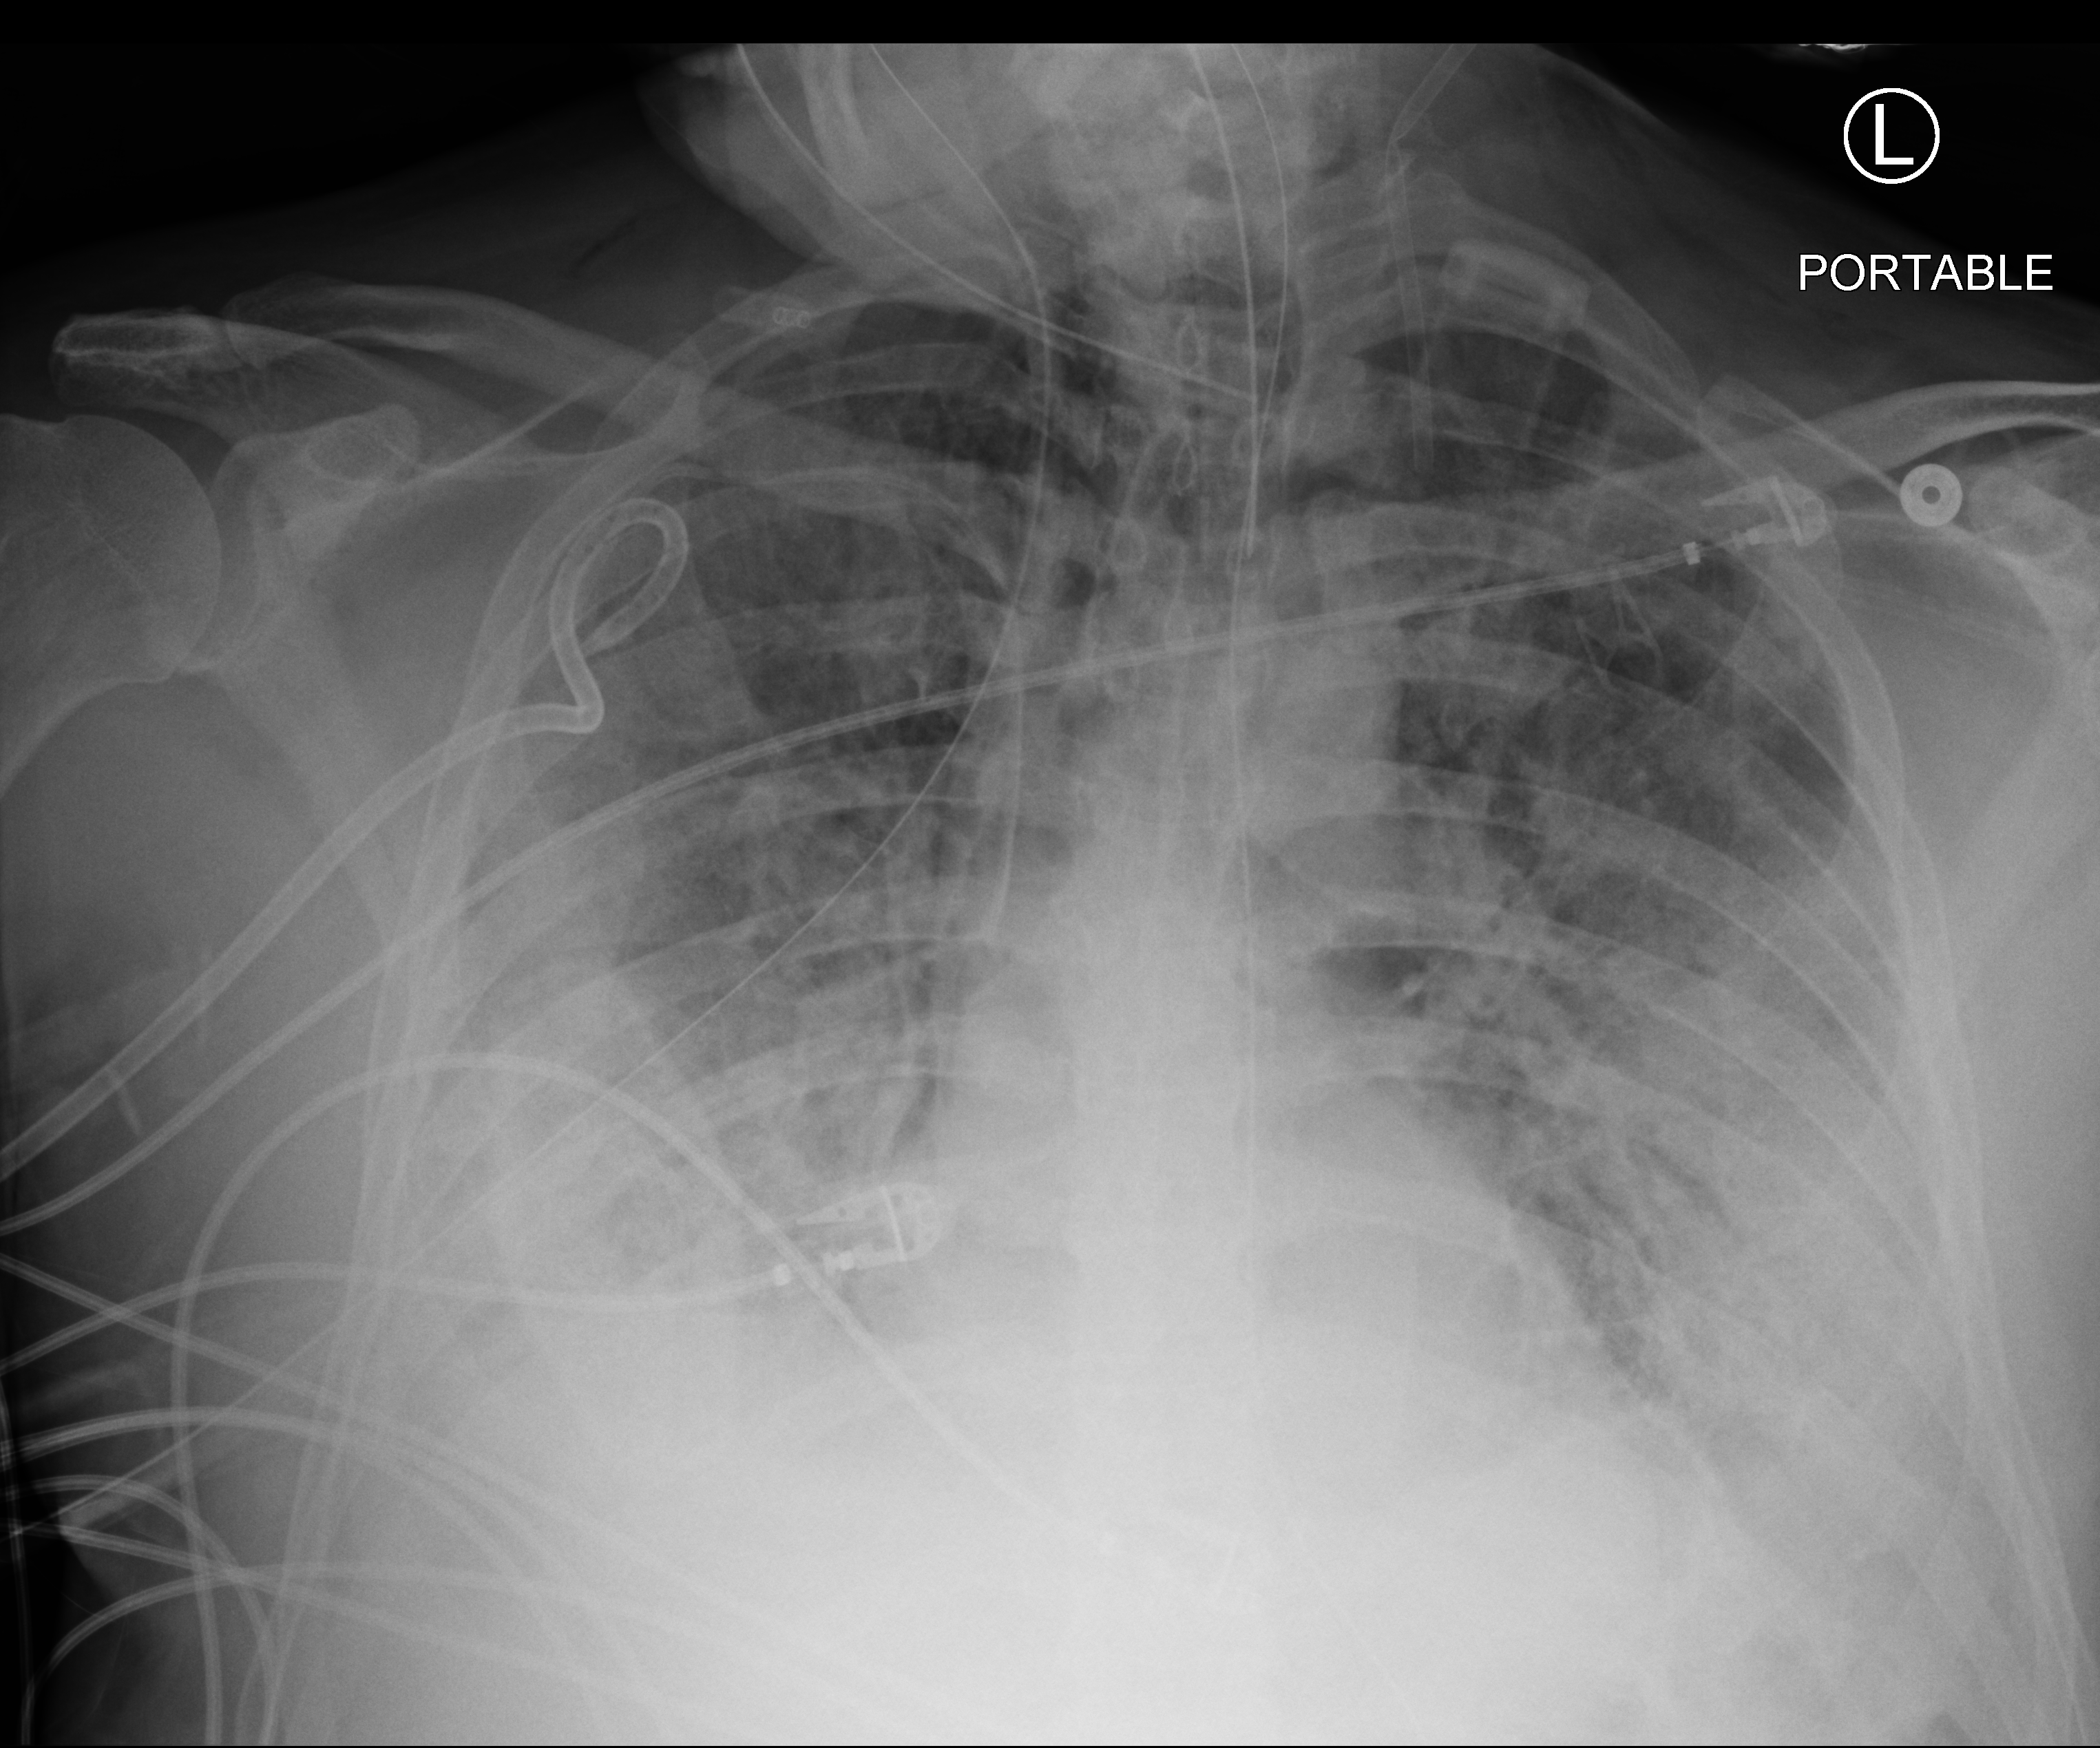
Portable chest radiograph, anteroposterior (AP) projection. Male patient hospitalised with COVID-19, age 60–74 years.
Admission-level facts for this patient (not findings on this image; timing relative to this image not recorded): diabetes (admission record): no.